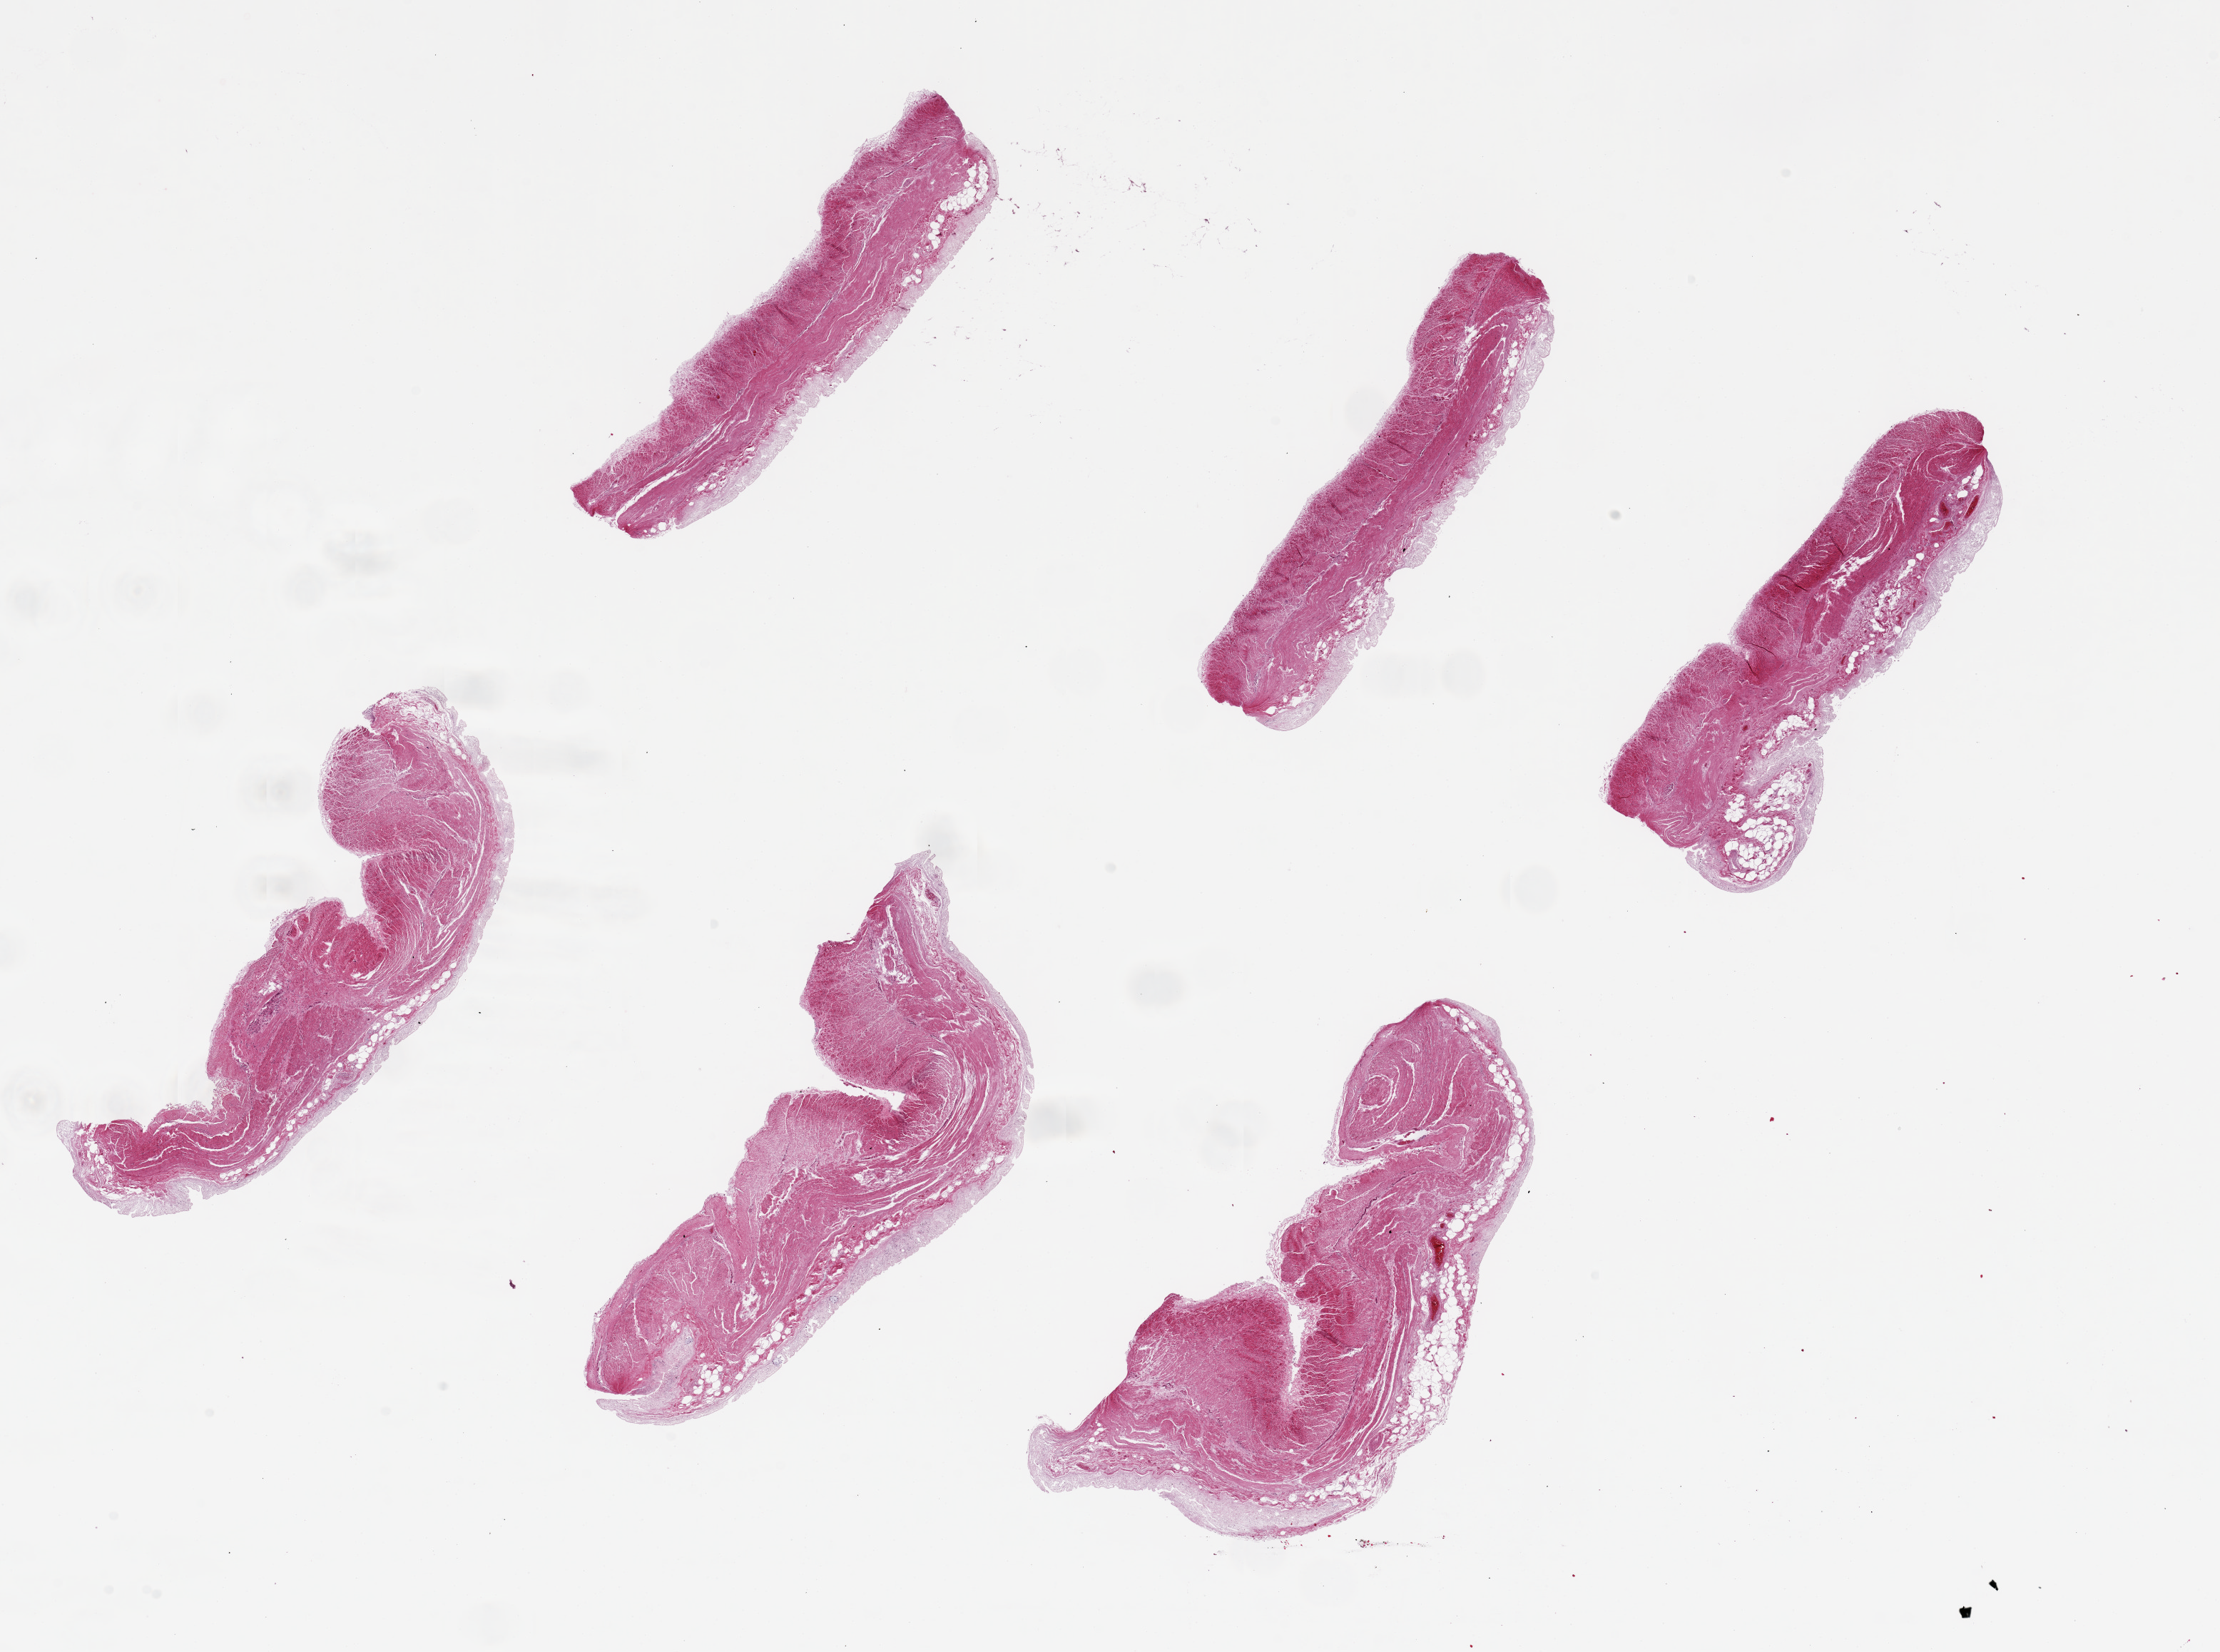
Digitized haematoxylin and eosin-stained section, a low-resolution overview of the entire scanned area, about 24.6 x 18.3 mm, PAXgene-fixed paraffin-embedded (PFPE) section, section of transverse colon (target tissue), donor tissue sample. Donor sex: female.
Review note (as recorded): 6 pieces, up to 7x3mm; badly autolyzed.